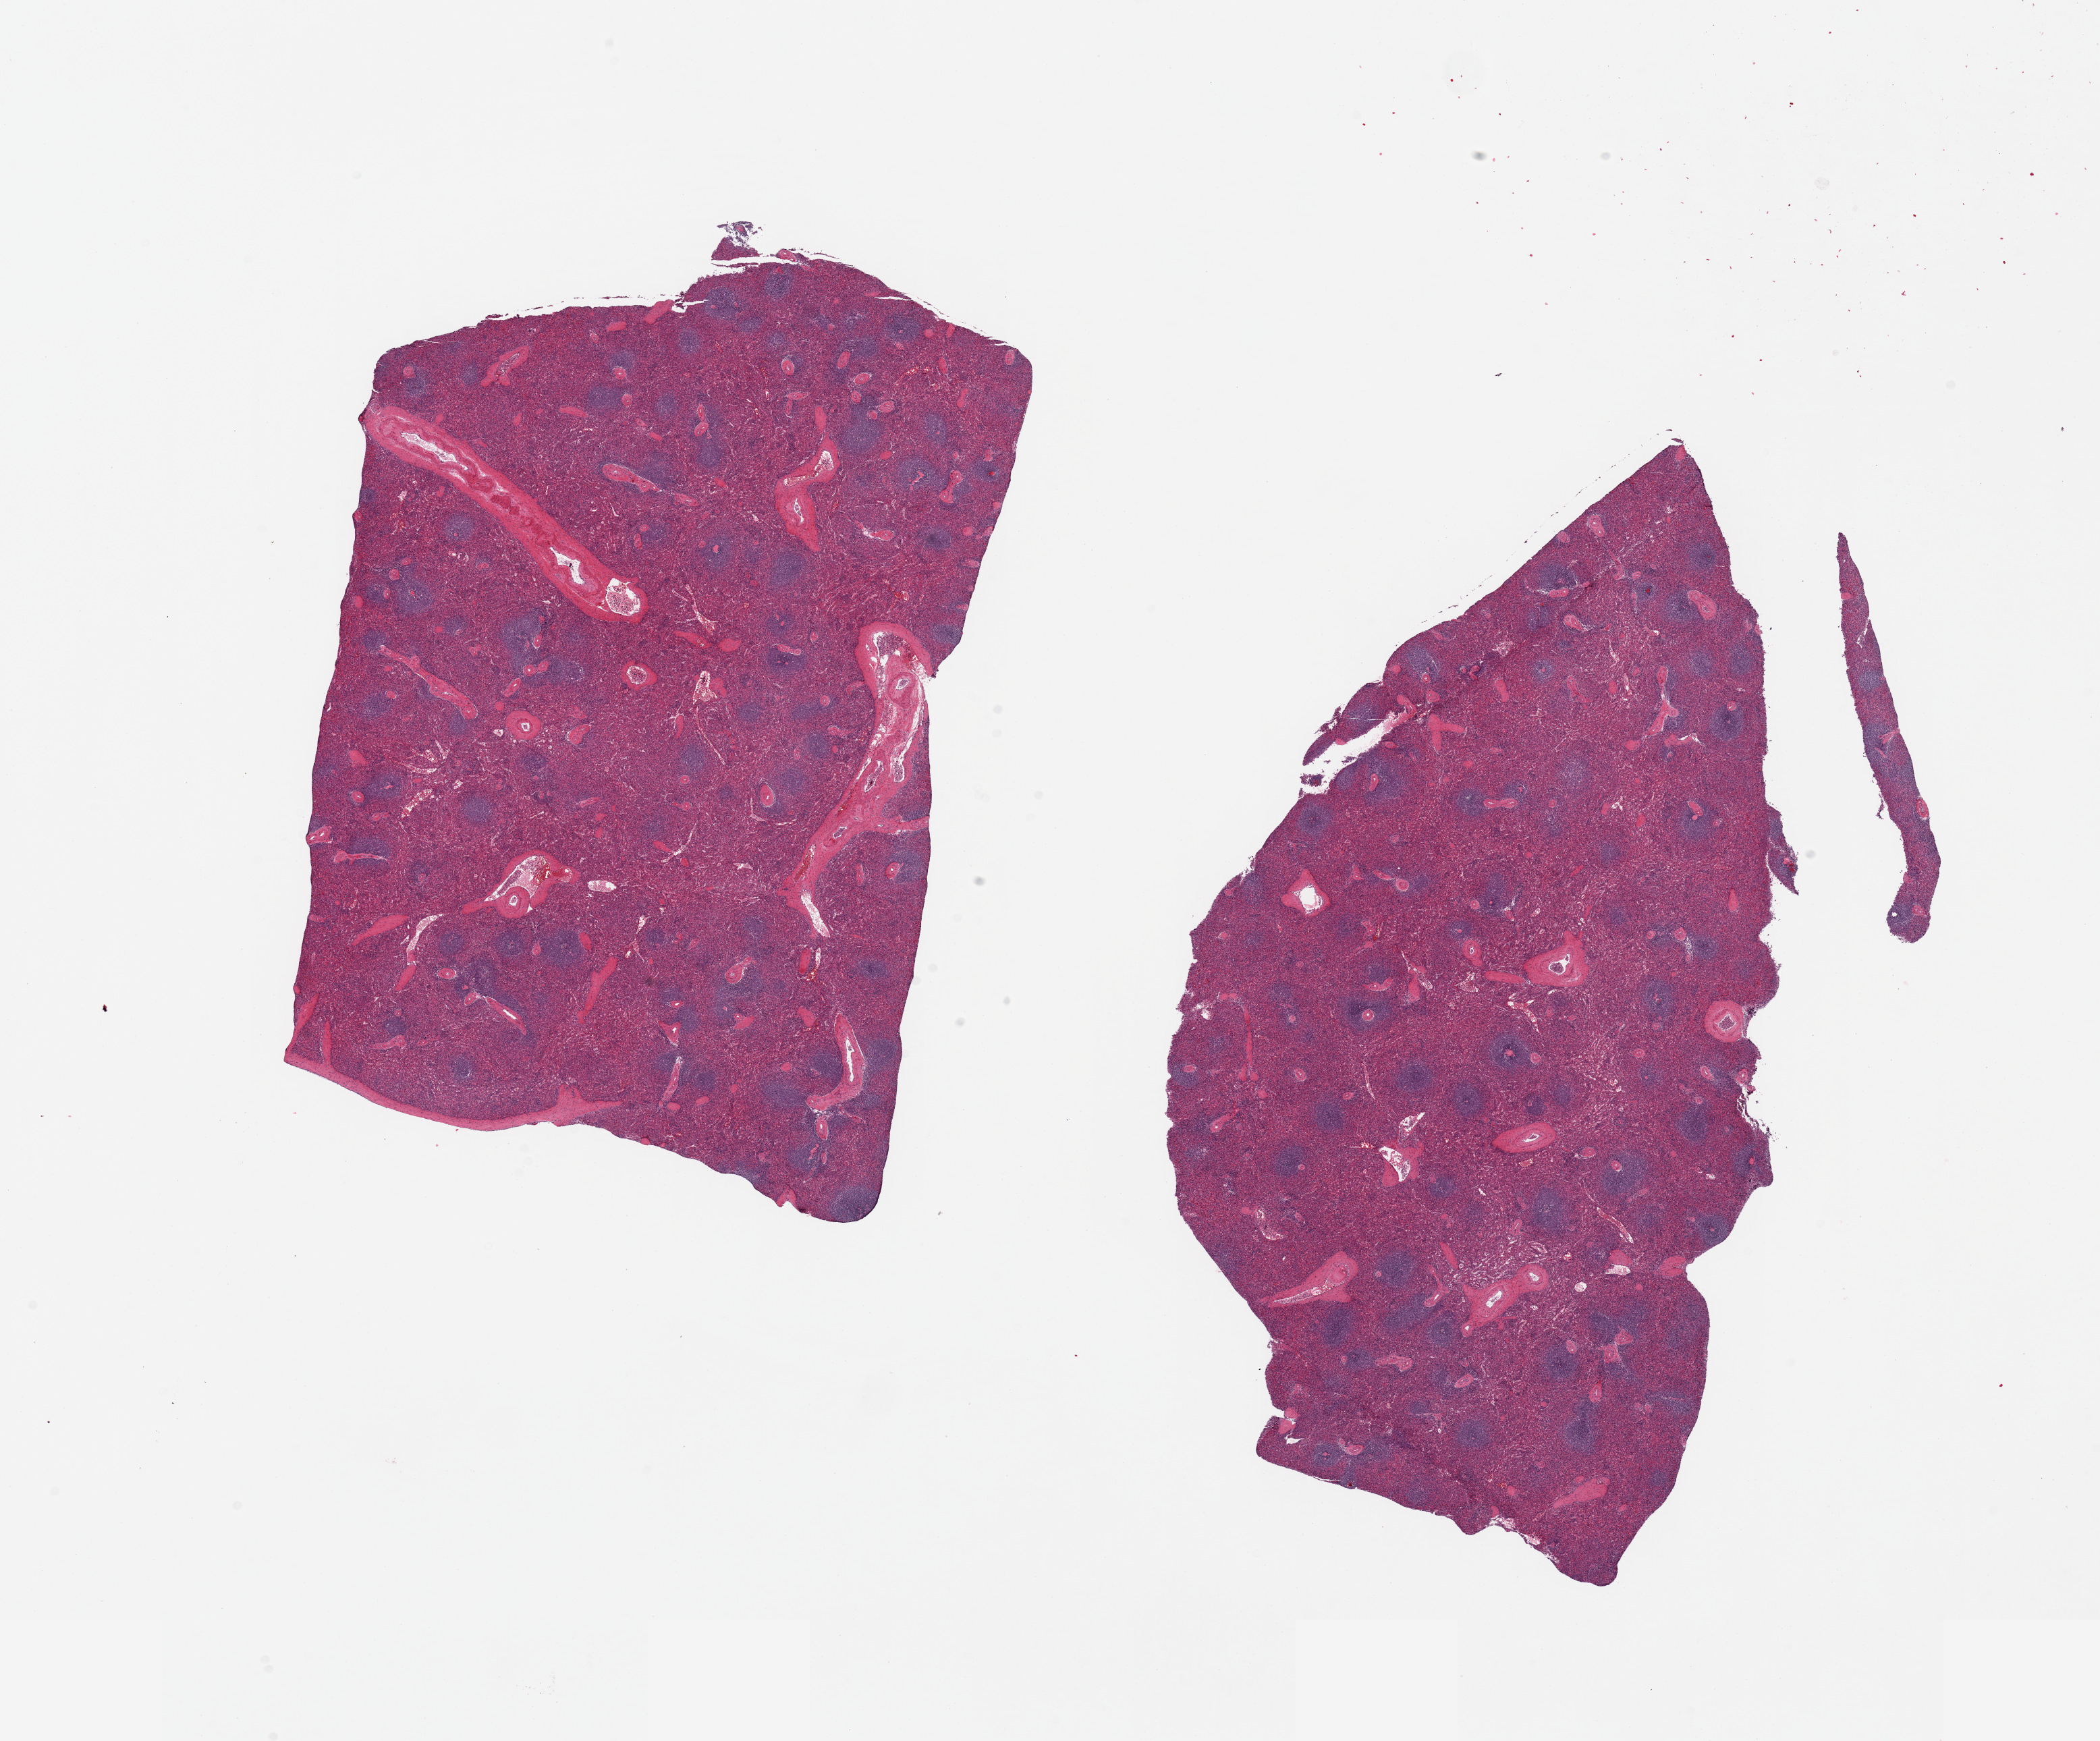
Whole-slide image, hematoxylin and eosin (H&E) stain — shown as a low-resolution overview of the whole scanned area (about 24.6 x 20.4 mm). PAXgene-fixed paraffin-embedded (PFPE) section. Sampled site (target tissue): spleen. Tissue donor sample.
Pathologist's review note for this sample: 2 pieces. 12x8 & 14x7mm; Not congested. Well defined lymphoid nodules.